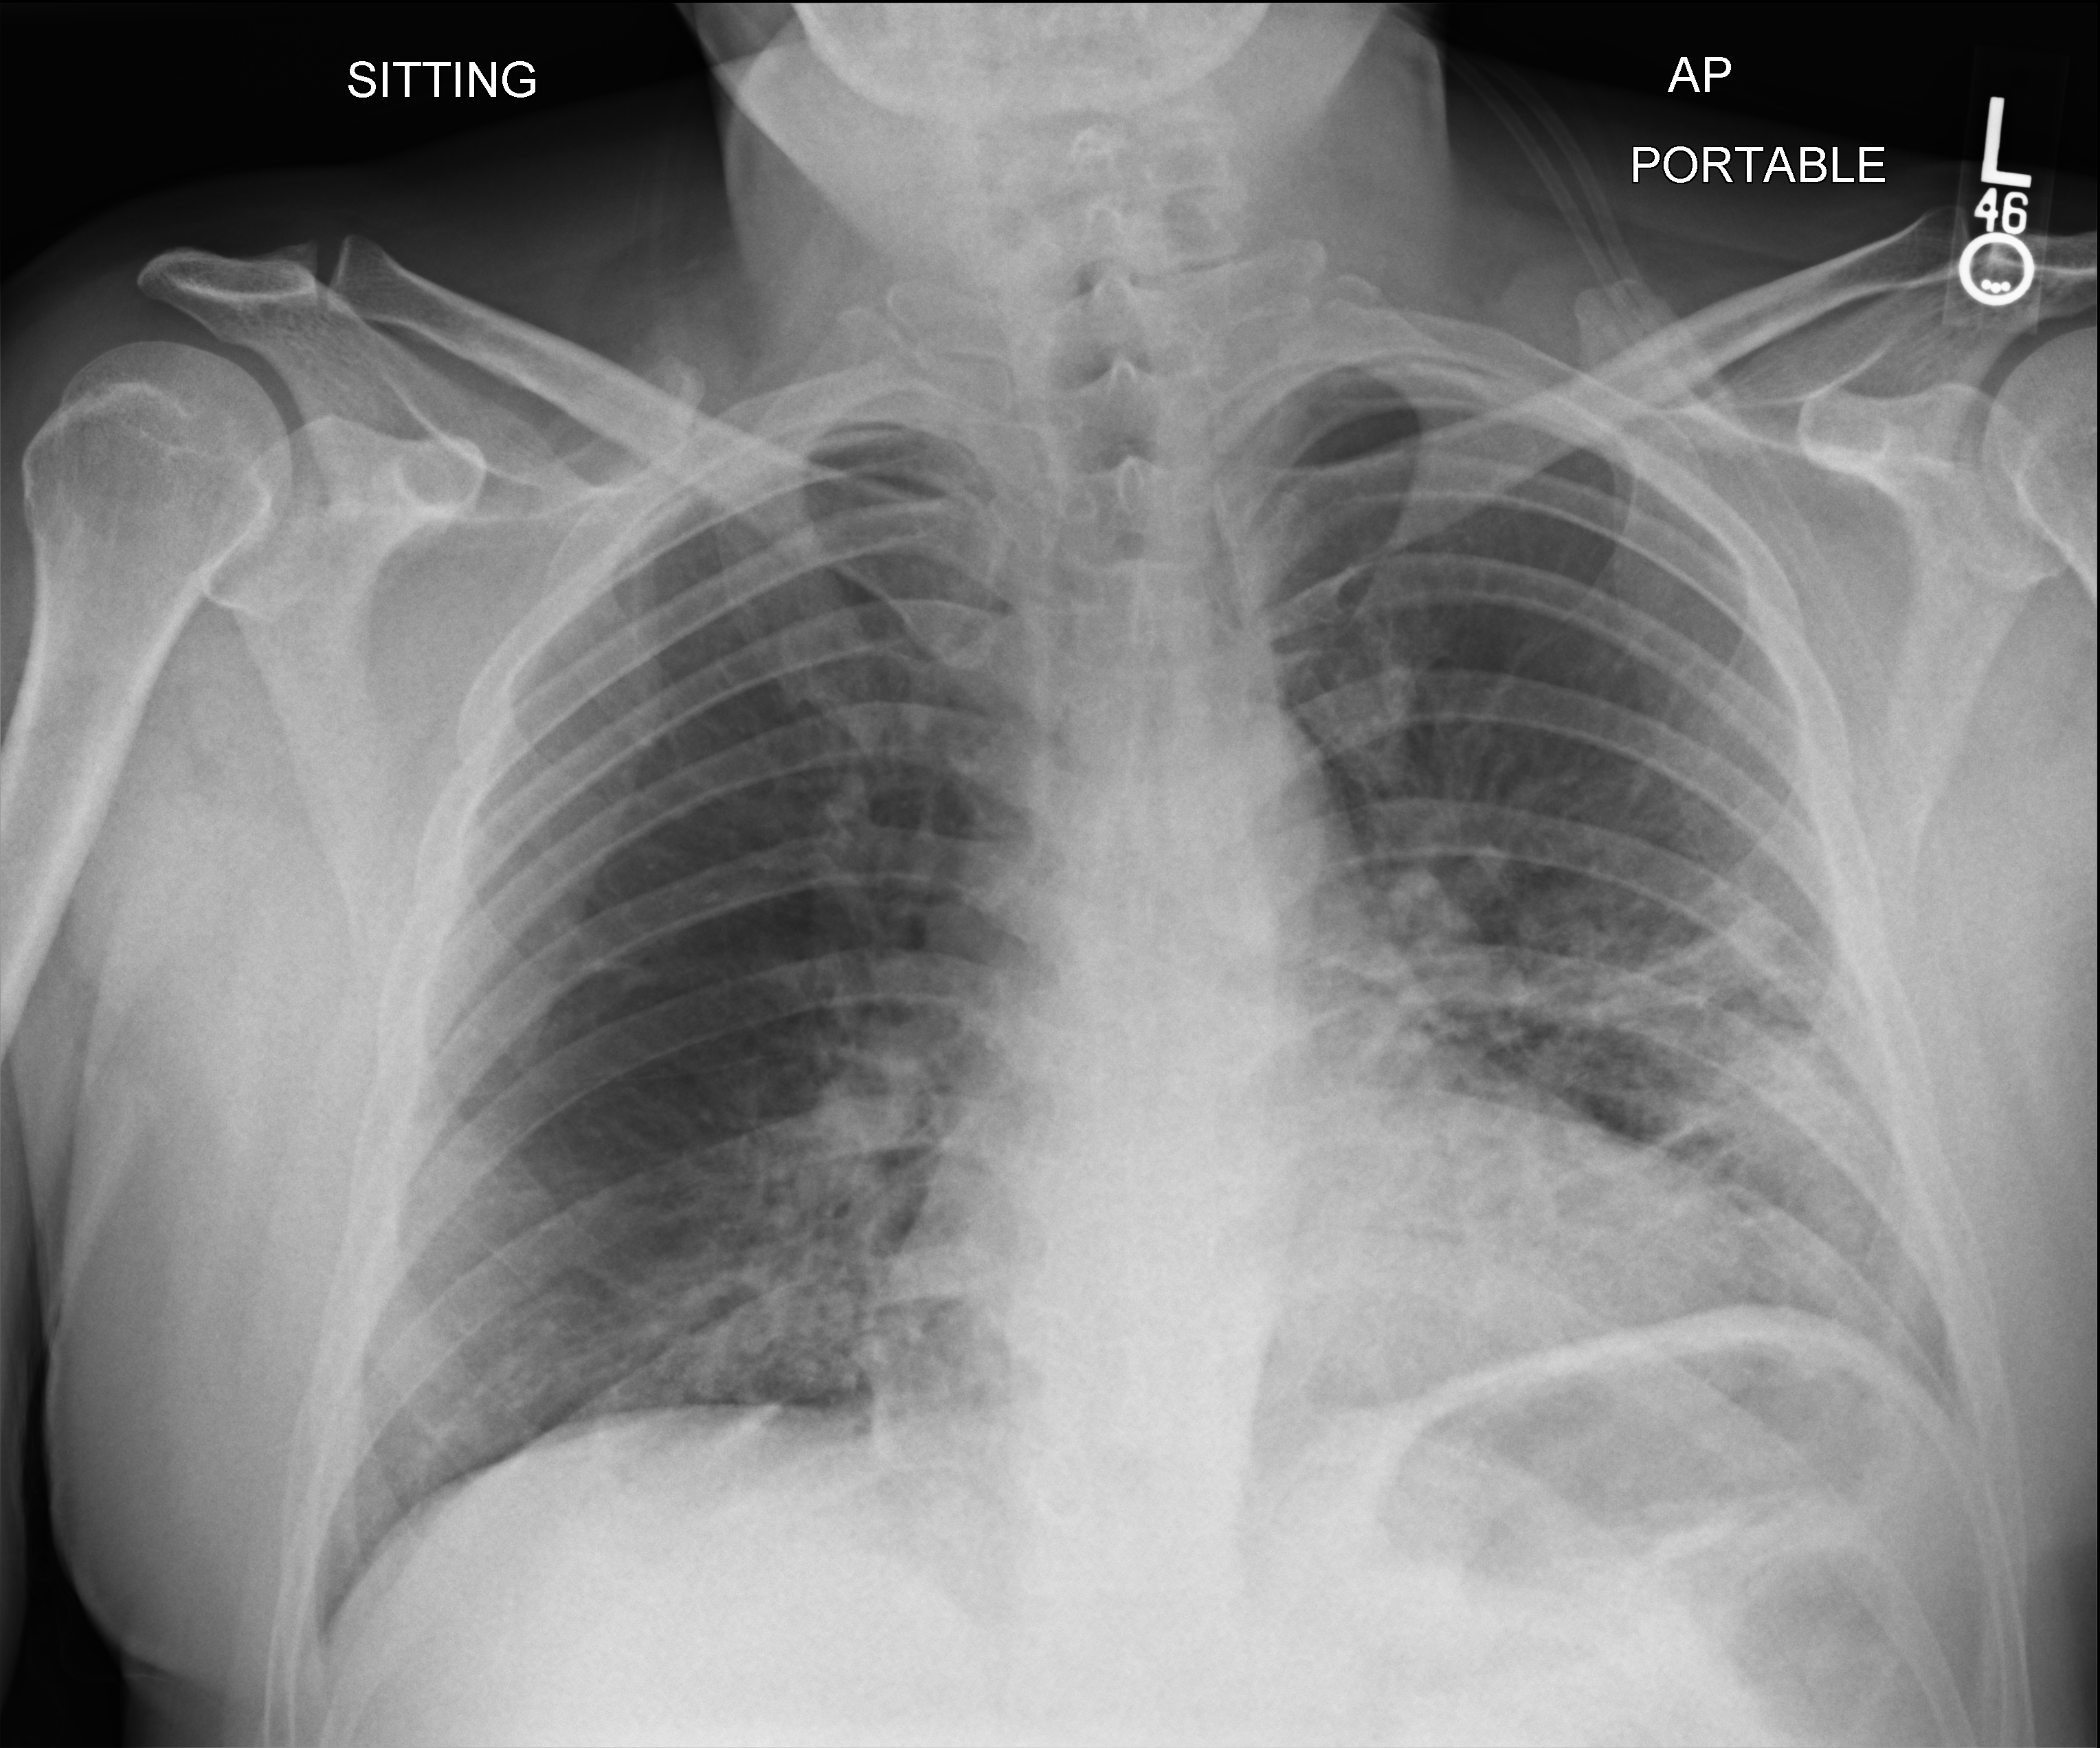
Portable chest radiograph, anteroposterior (AP) projection. Patient hospitalised with COVID-19; male, aged 18–59 years.
From the hospital-stay record, not from the radiograph (when in the stay this image was taken is not recorded):
- COPD (admission record): no
- mechanically ventilated during this hospital stay: no